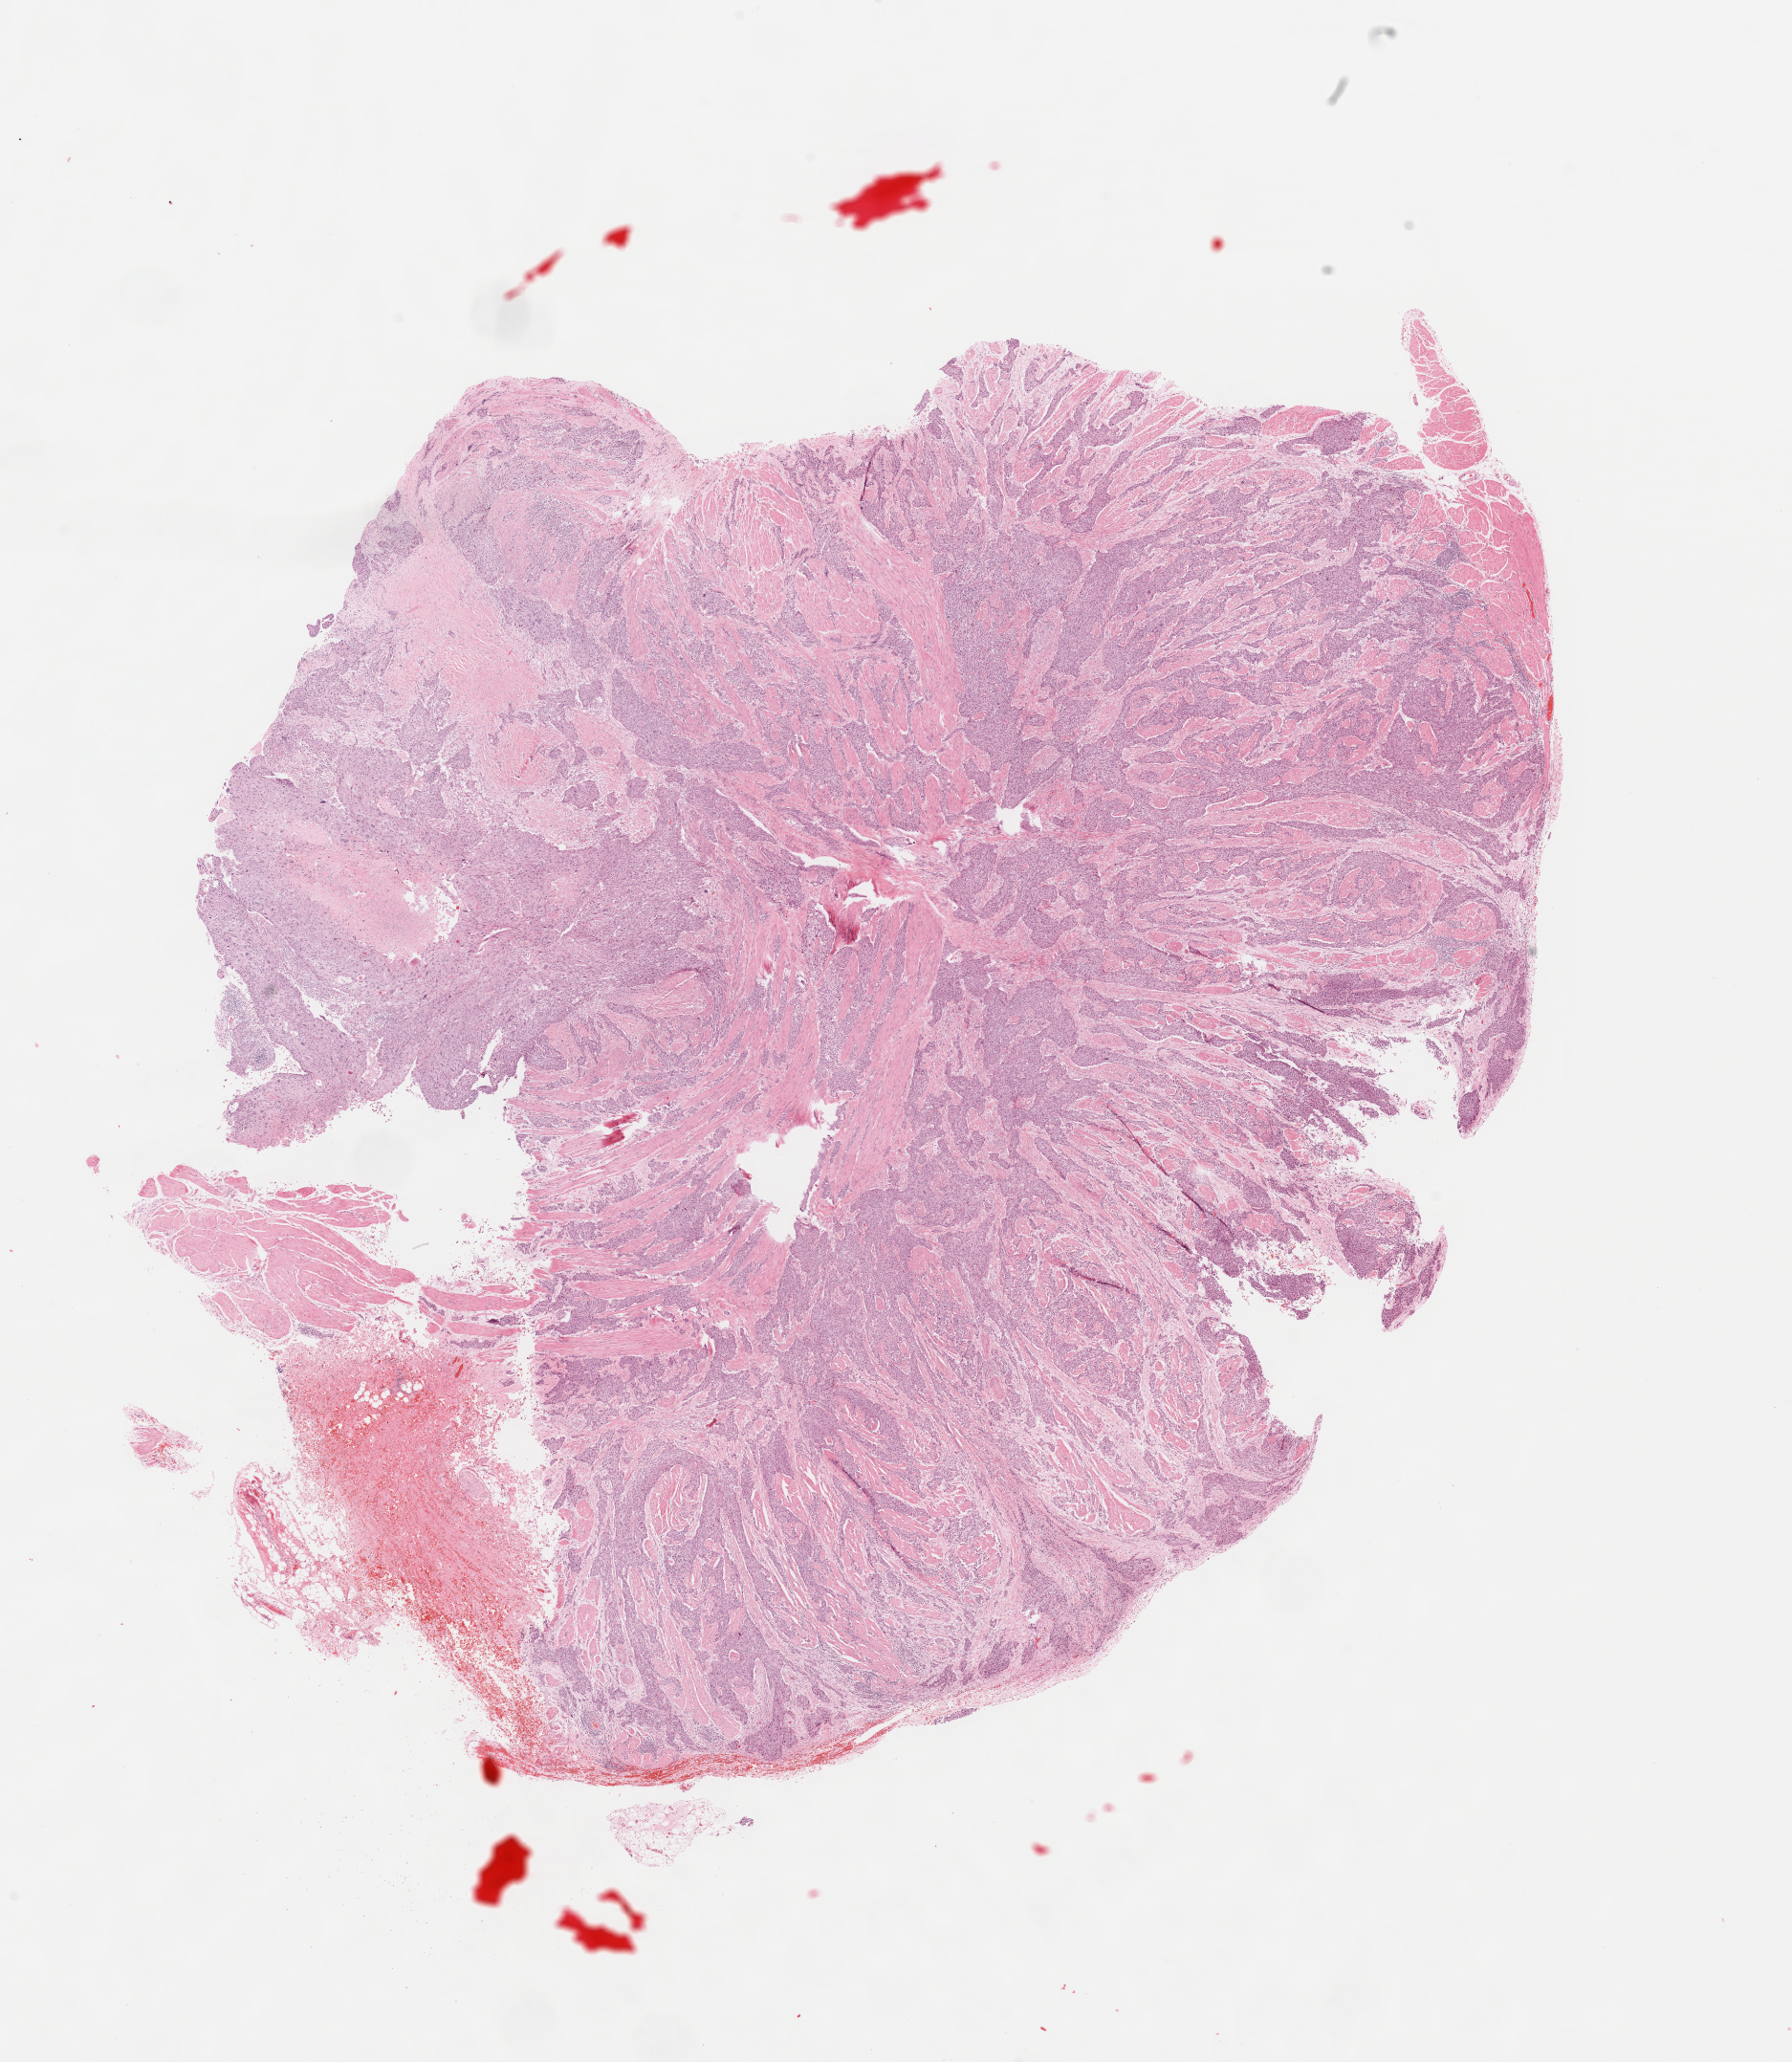
Whole-slide histology image, H&E-stained, whole scanned area (about 14.8 x 17.0 mm, from a 40x scan) shown as a low-resolution overview. FFPE section. Sample: primary tumour, esophagus. Patient: male, age at initial diagnosis 61 years. Histologic grade: G2 (moderately differentiated).
- histologic diagnosis: Squamous cell carcinoma, NOS (lower third of esophagus)
- AJCC pathologic stage: IIIA (7th edition)
- lymph nodes positive (case pathology): 1 of 3 examined